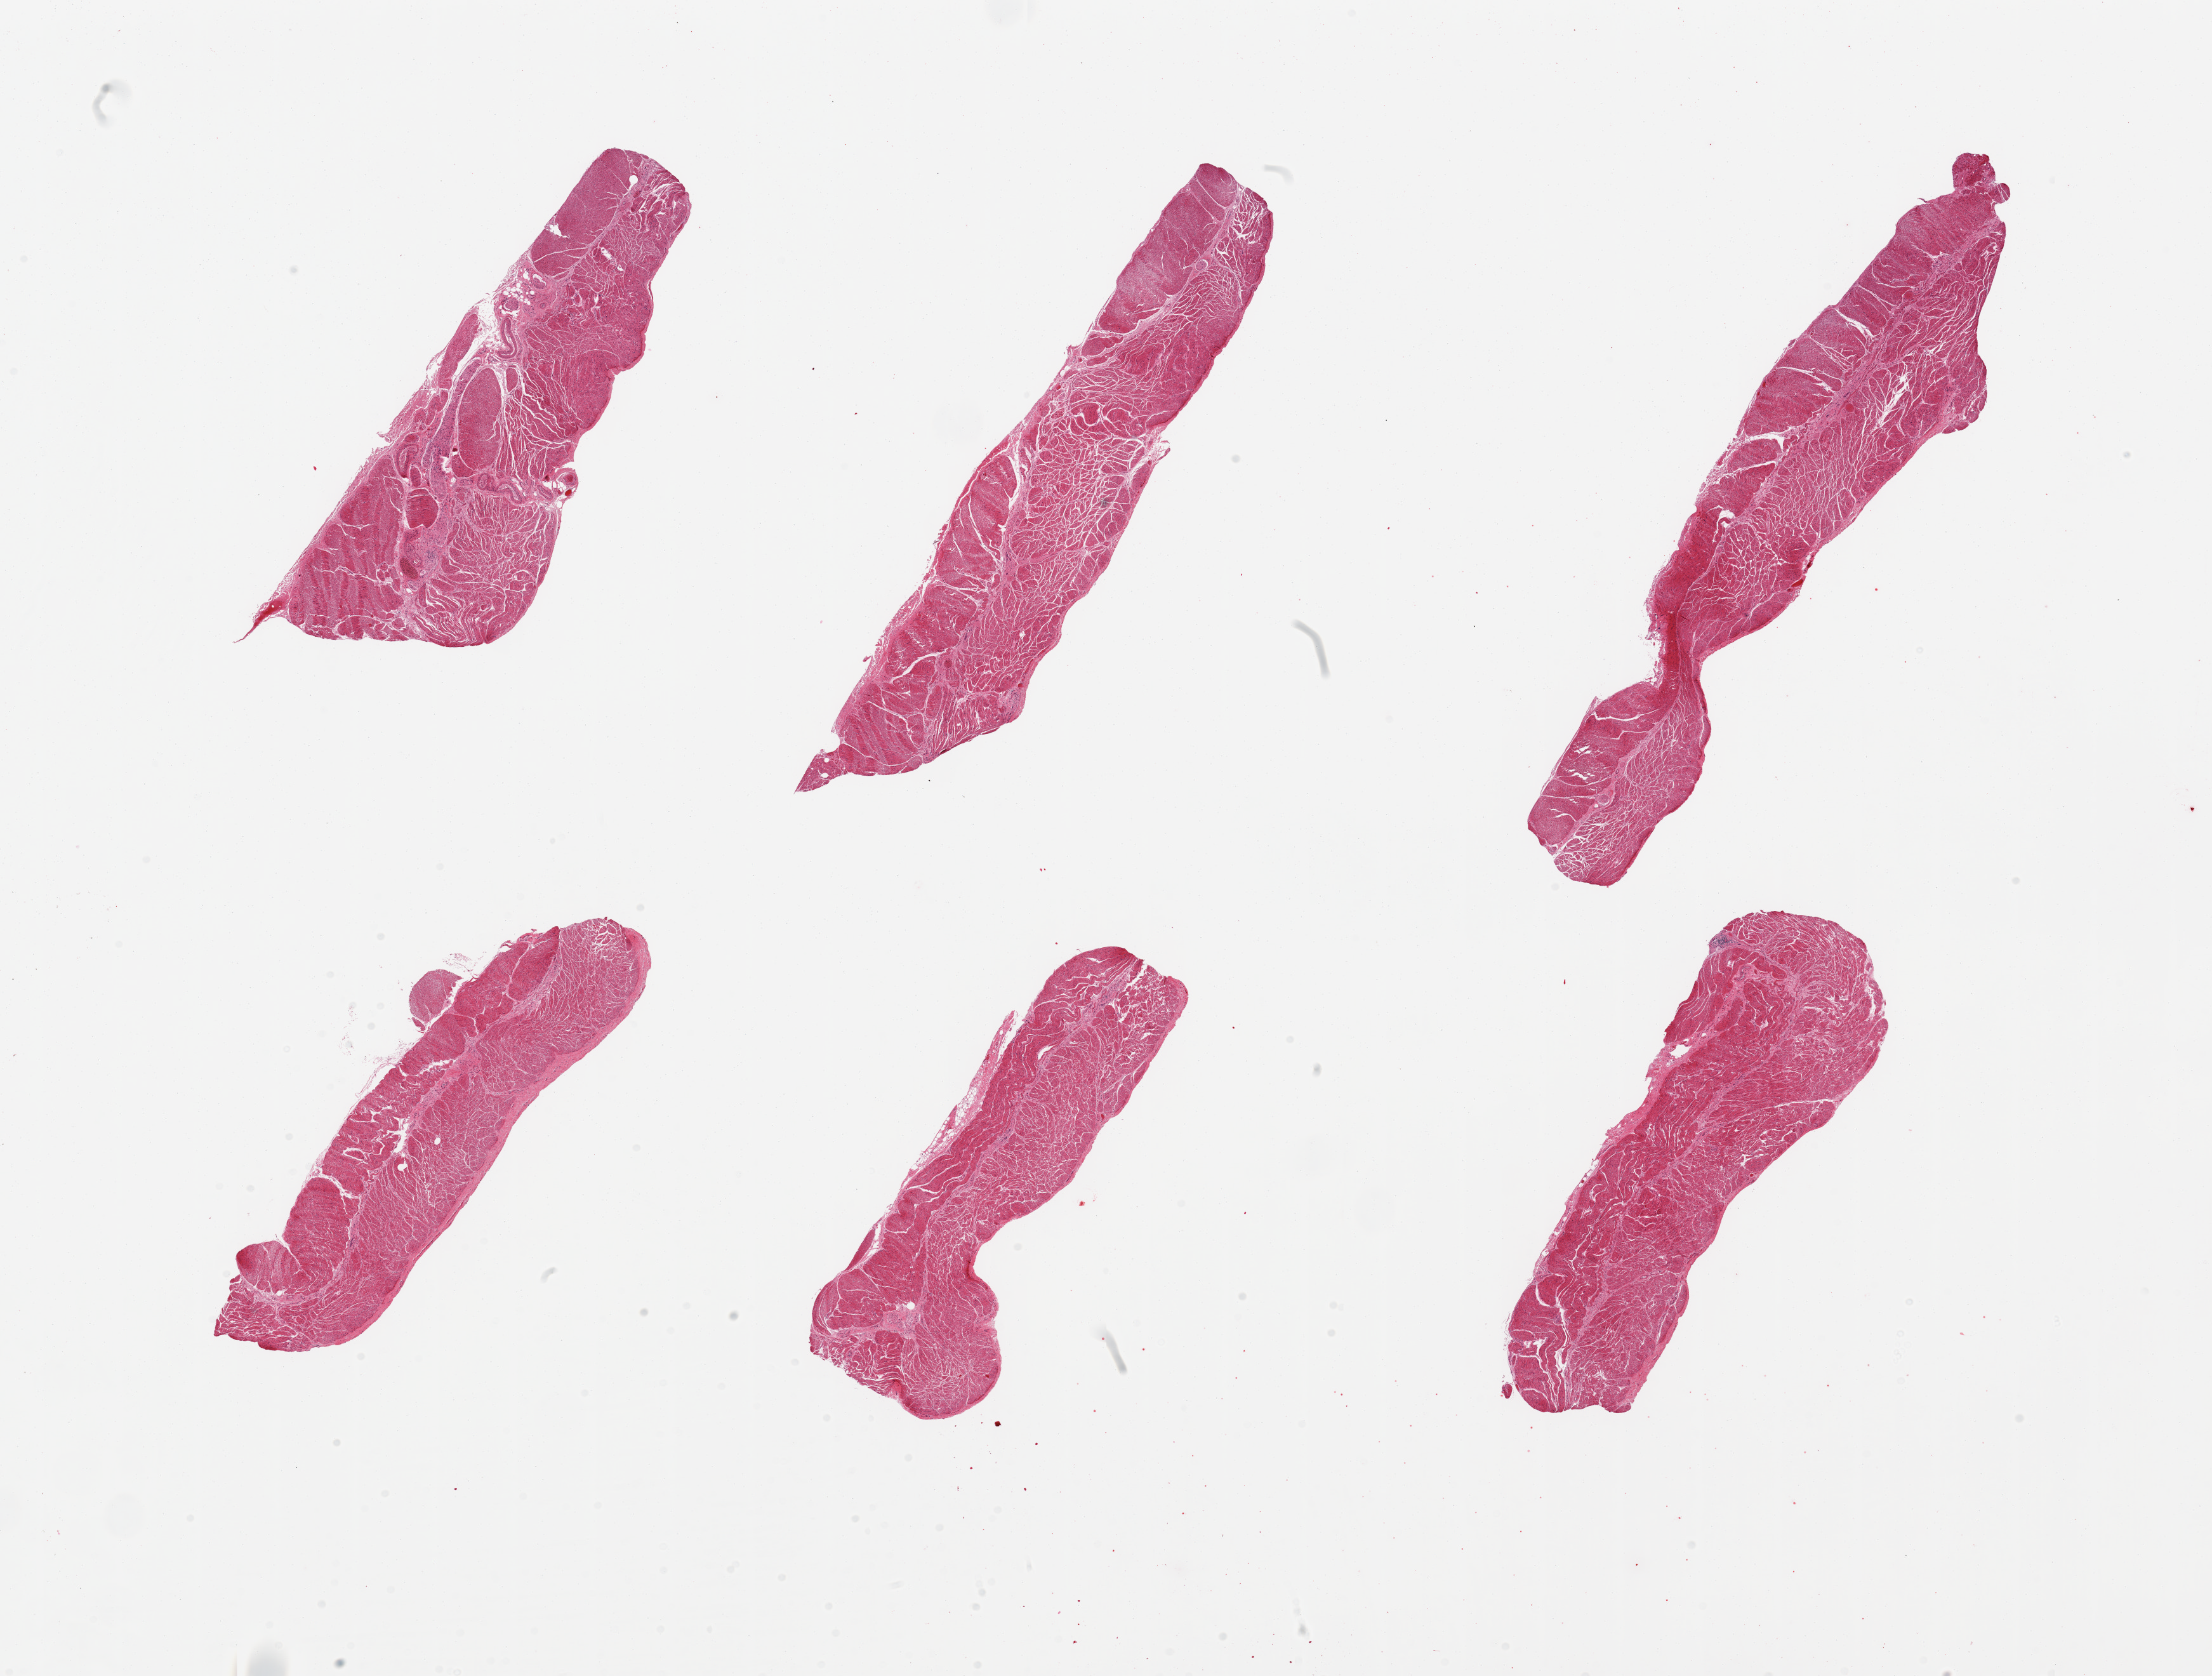
Digitized haematoxylin and eosin-stained section, brightfield, whole scanned area (about 27.6 x 20.9 mm, slide scanned at 20x) shown as a low-resolution overview. PAXgene-fixed paraffin-embedded (PFPE) section. Section of esophageal muscle (target tissue). Tissue donor sample.
Pathologist's review note for this sample: 6 pieces; target muscularis well trimmed.